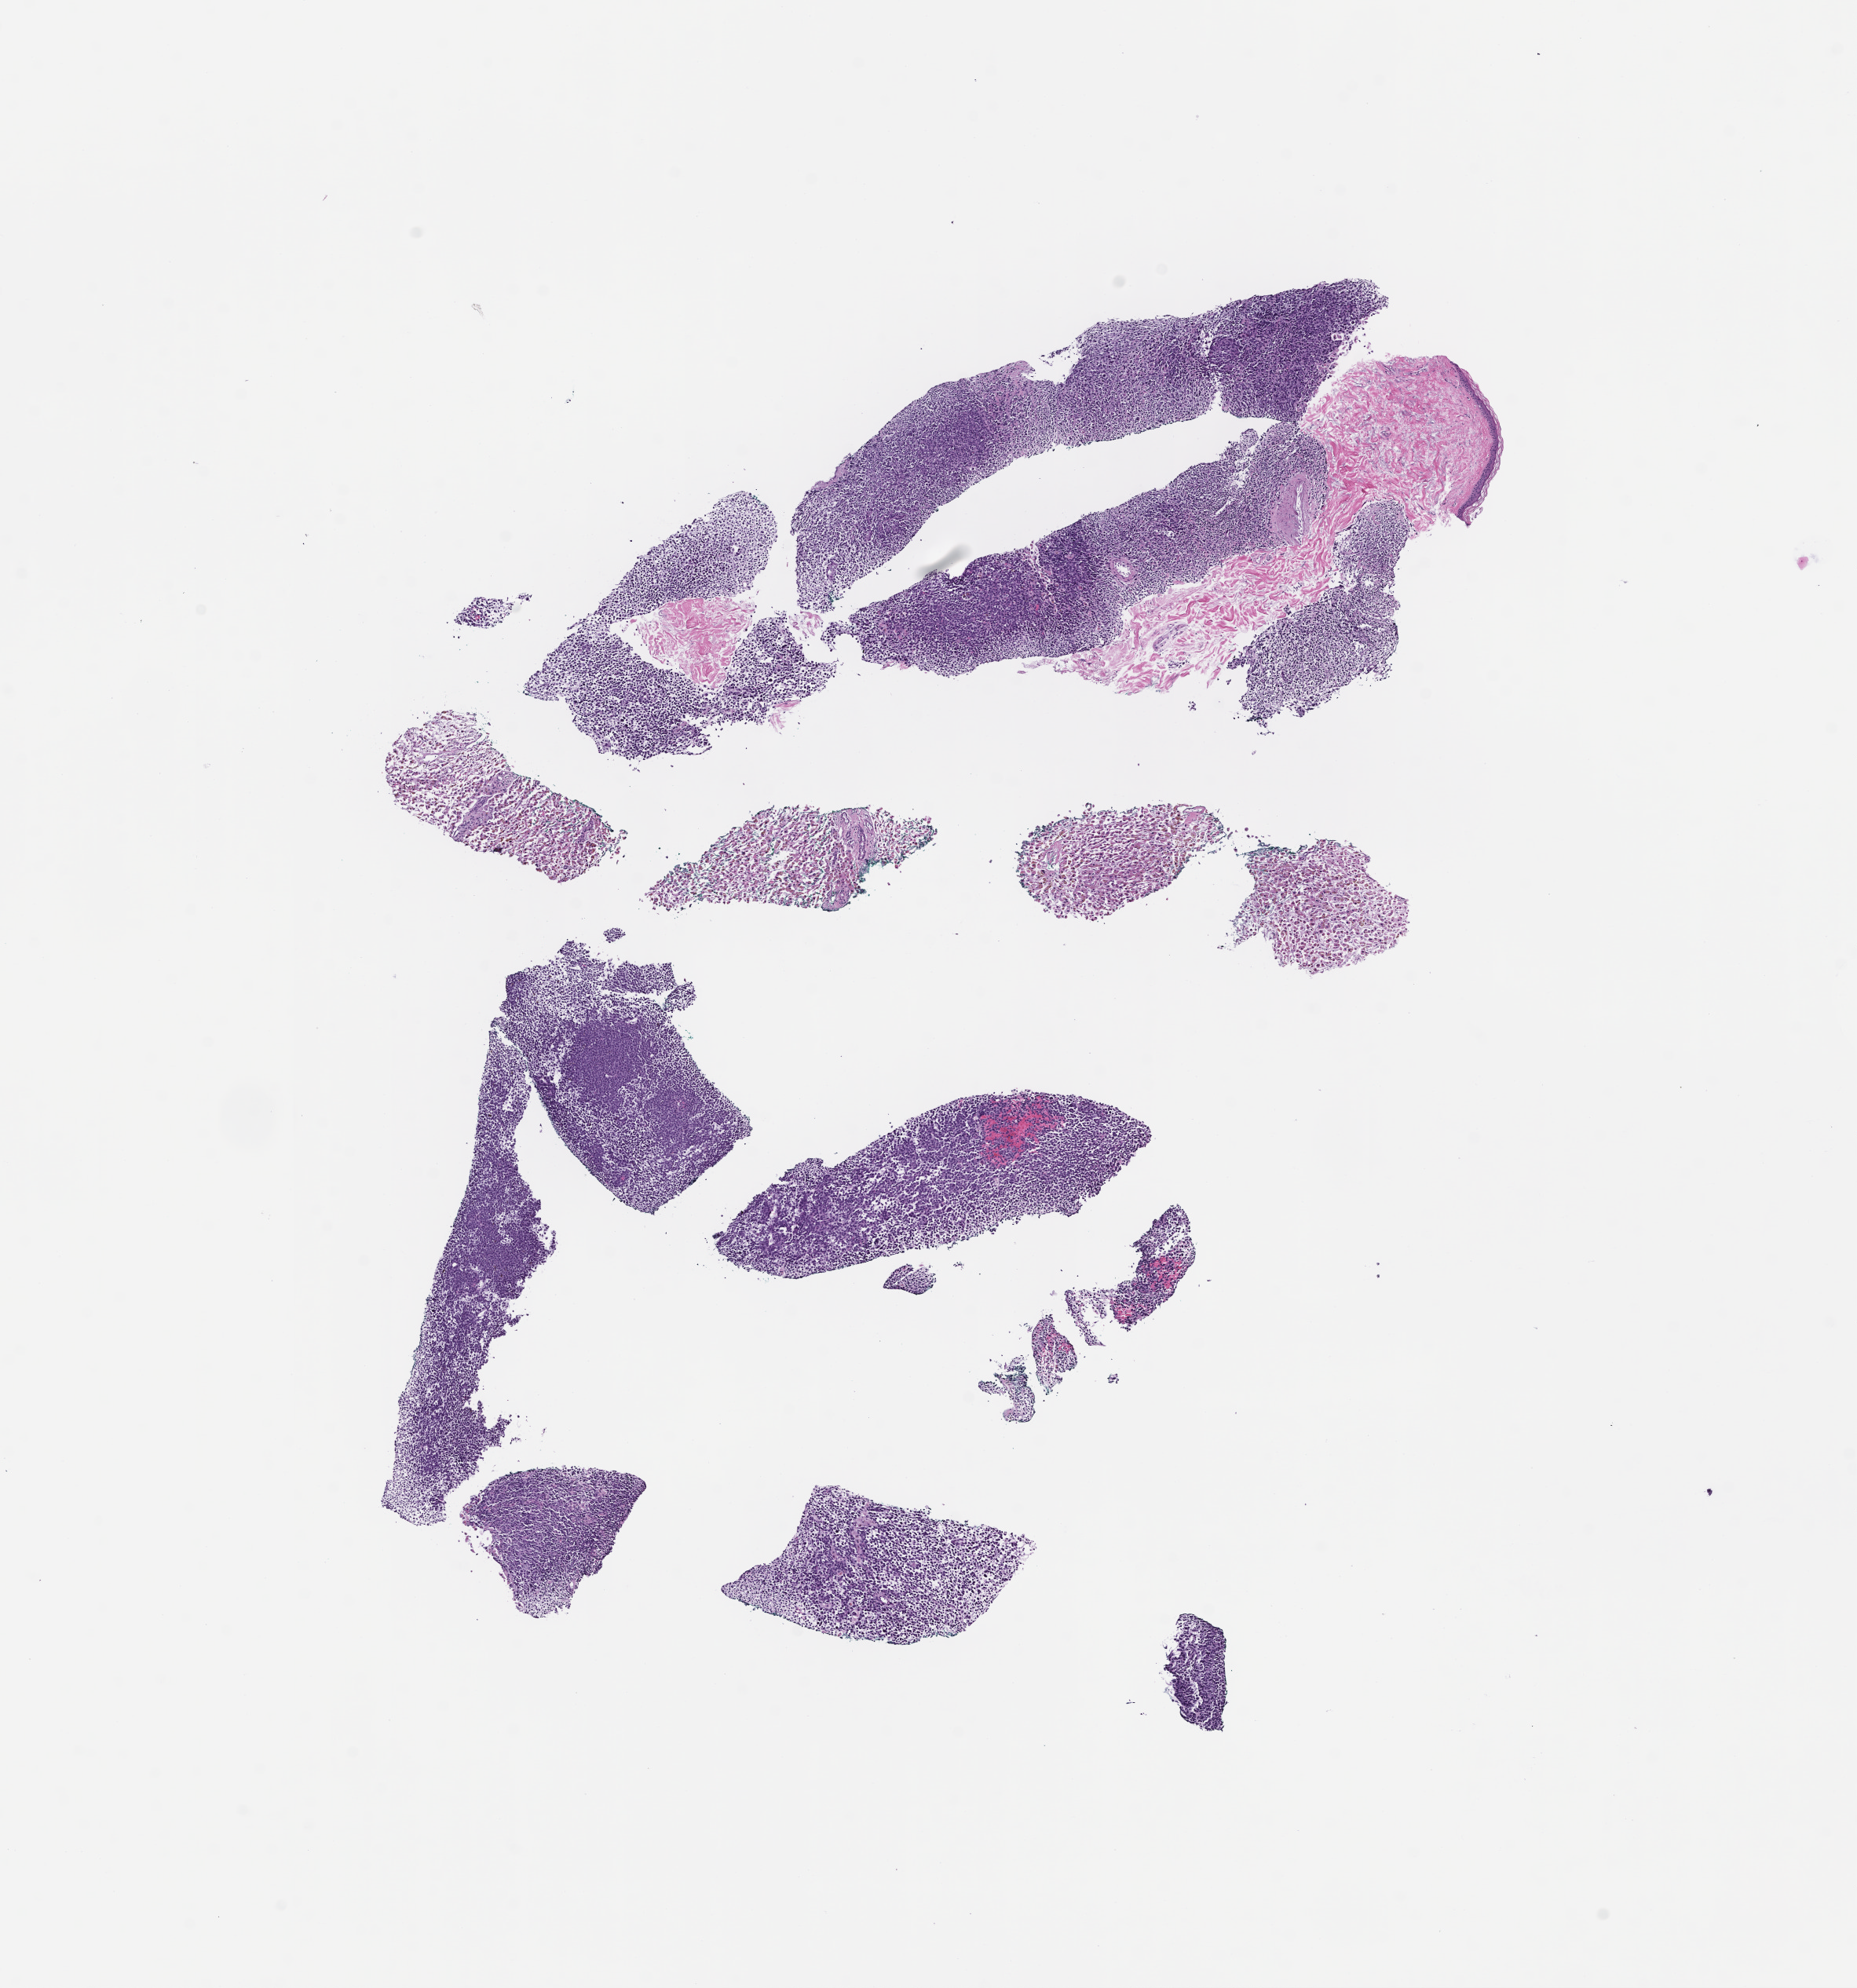
H&E whole-slide image — low-resolution overview of the scanned area, about 9.5 x 10.2 mm; formalin-fixed, paraffin-embedded (FFPE) tissue. Patient: male.
This section: metastasis (sampled organ not recorded). Patient diagnosis (primary): Melanoma.